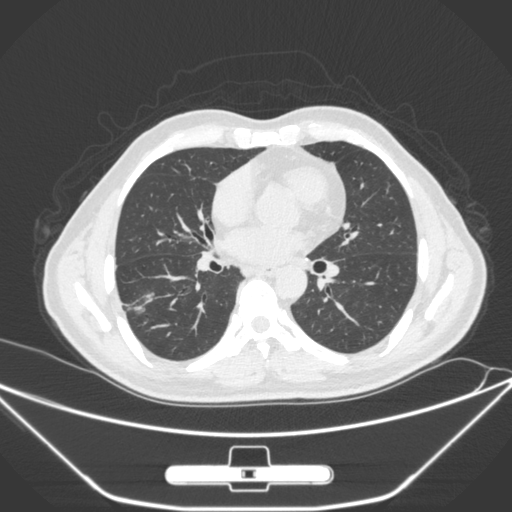
Chest CT, one axial slice; position 140 of 310 along the scan axis; 120 kVp; lung window (W 1500 / L -600 HU); 1 mm slice thickness; 512 × 512 image matrix. Male patient, age 71 years. Case-level facts recorded for this patient, not image findings: clinical TNM (as recorded): T1c N0 M0.
Structures marked on this image (rectangle marked by the reading radiologist):
- lung tumour (recorded histology: adenocarcinoma): bounding box <119,285,156,320> (left, top, right, bottom; pixels)